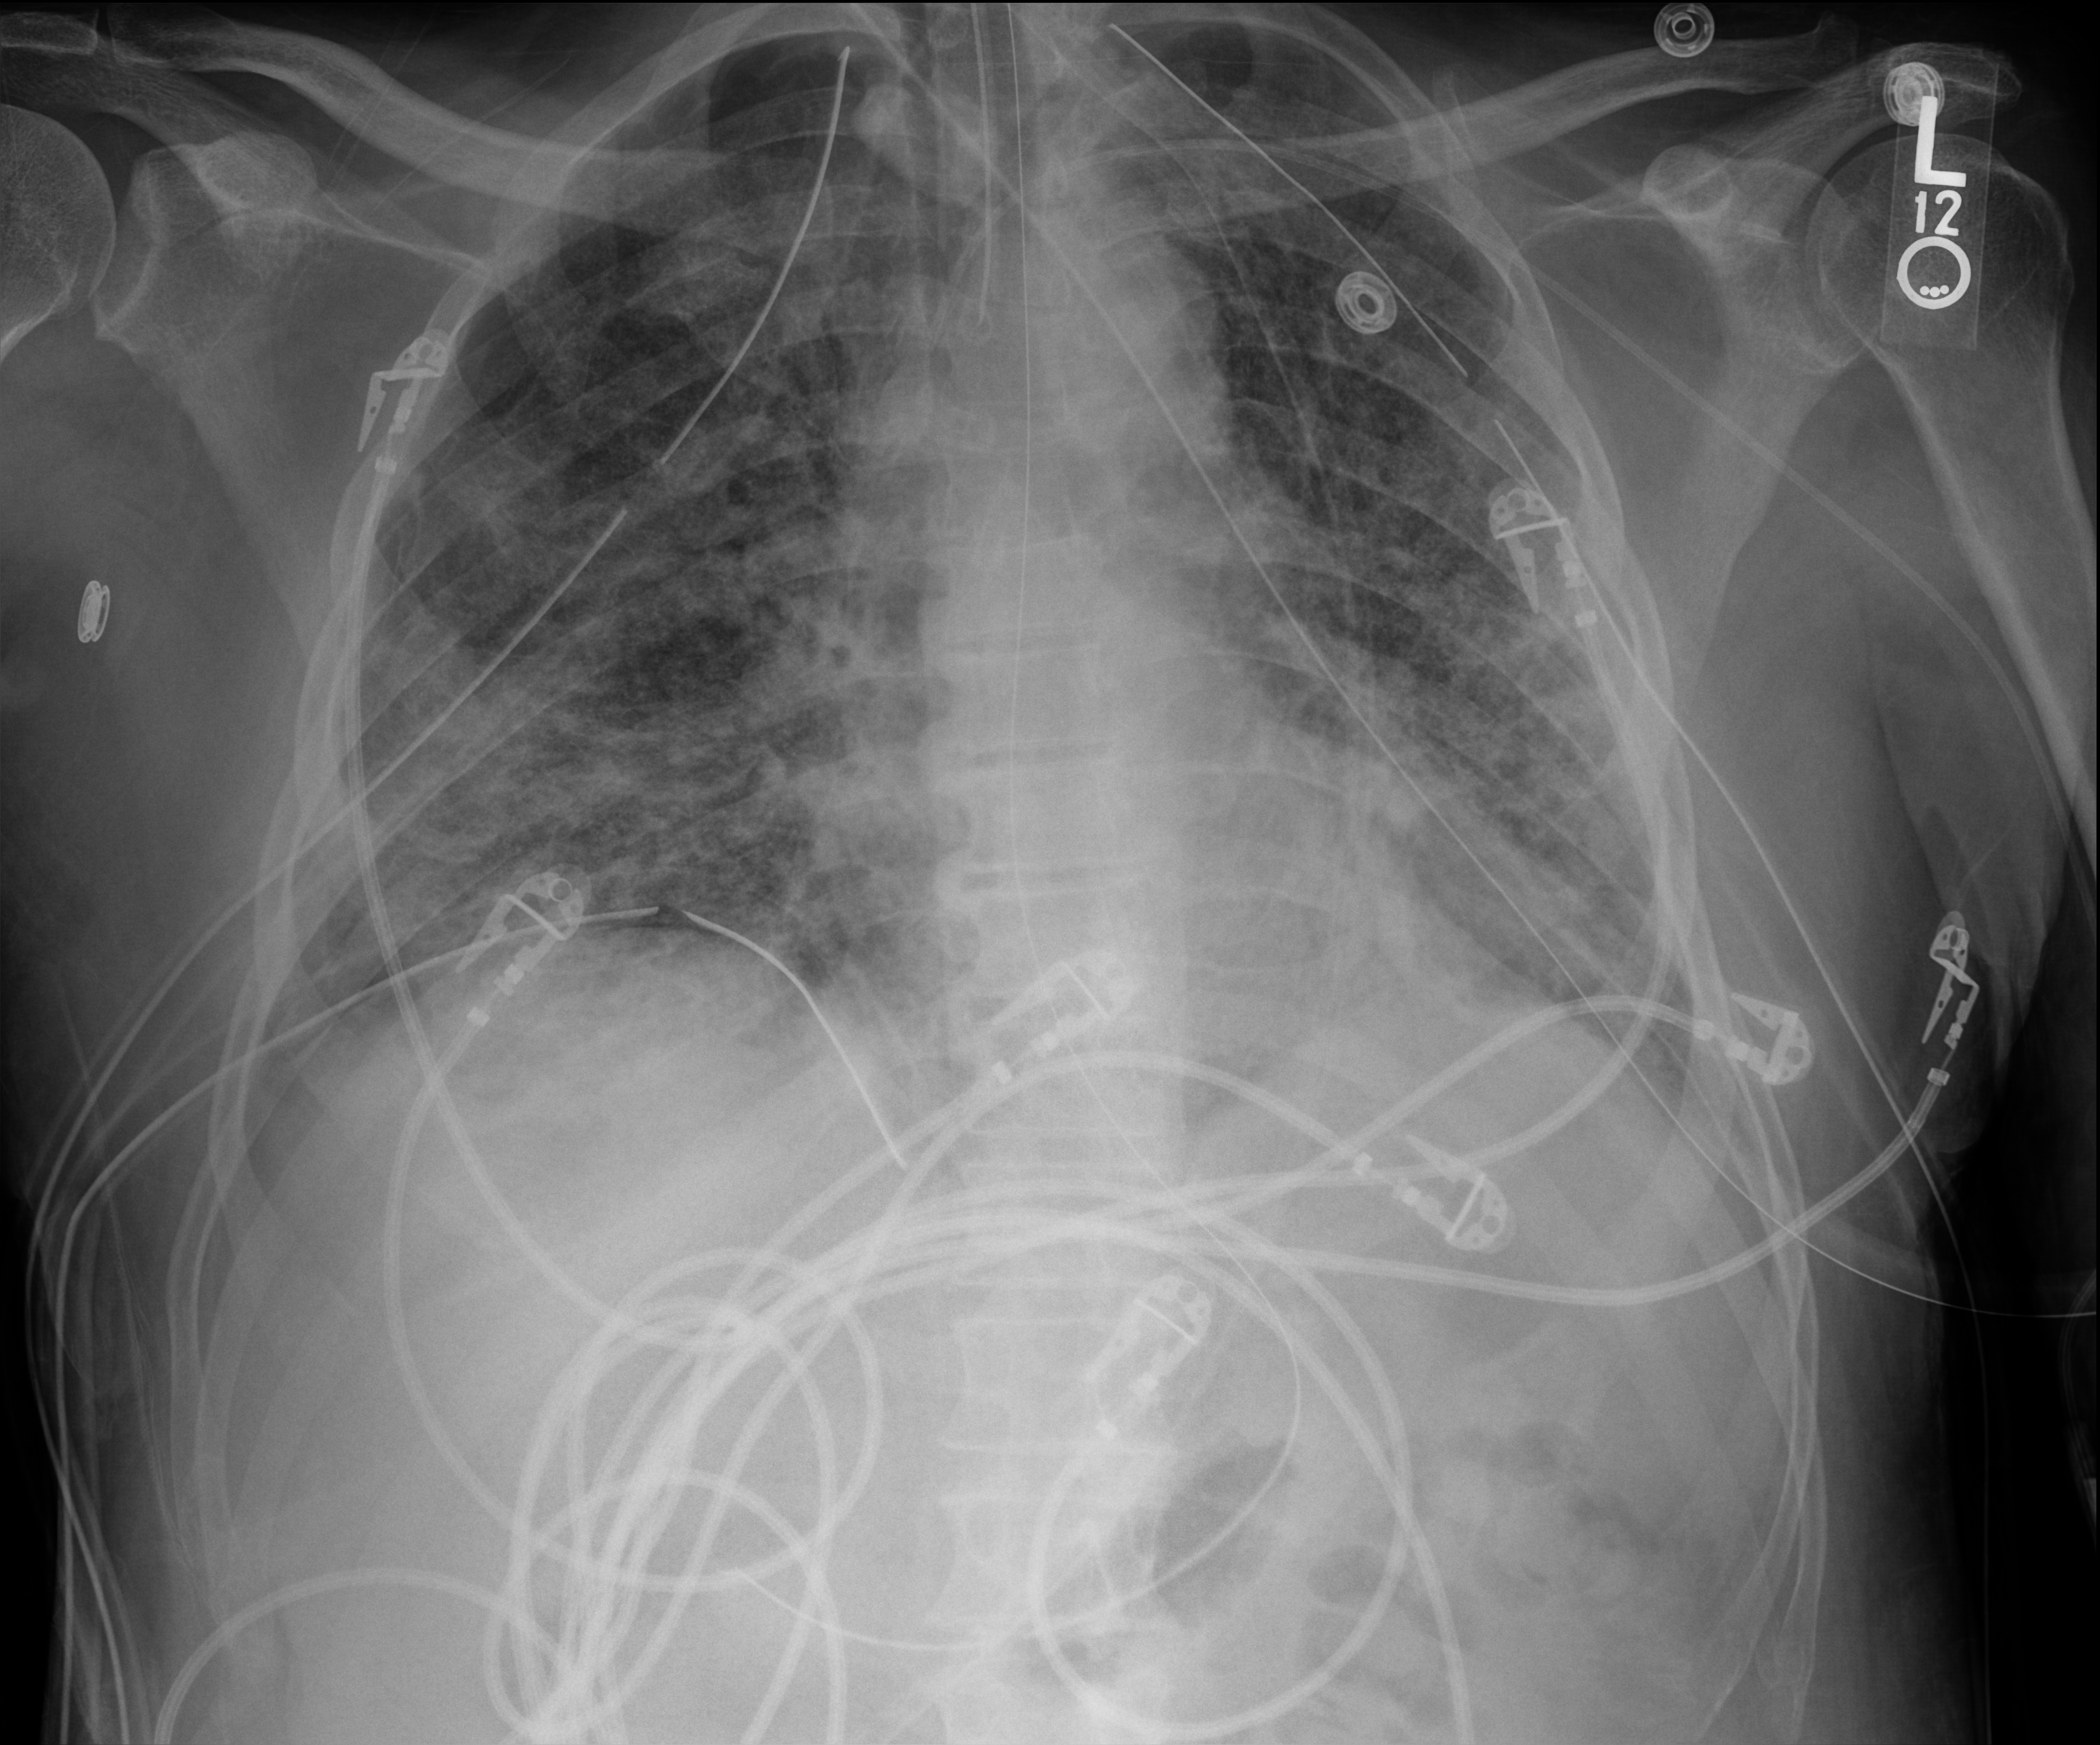
Portable chest radiograph, anteroposterior (AP) projection. Patient hospitalised with COVID-19; male, aged 18–59 years.
Admission-level facts for this patient (not findings on this image; timing relative to this image not recorded): length of hospital stay: 83 days; admitted to intensive care during this hospital stay: yes; mechanically ventilated during this hospital stay: yes.